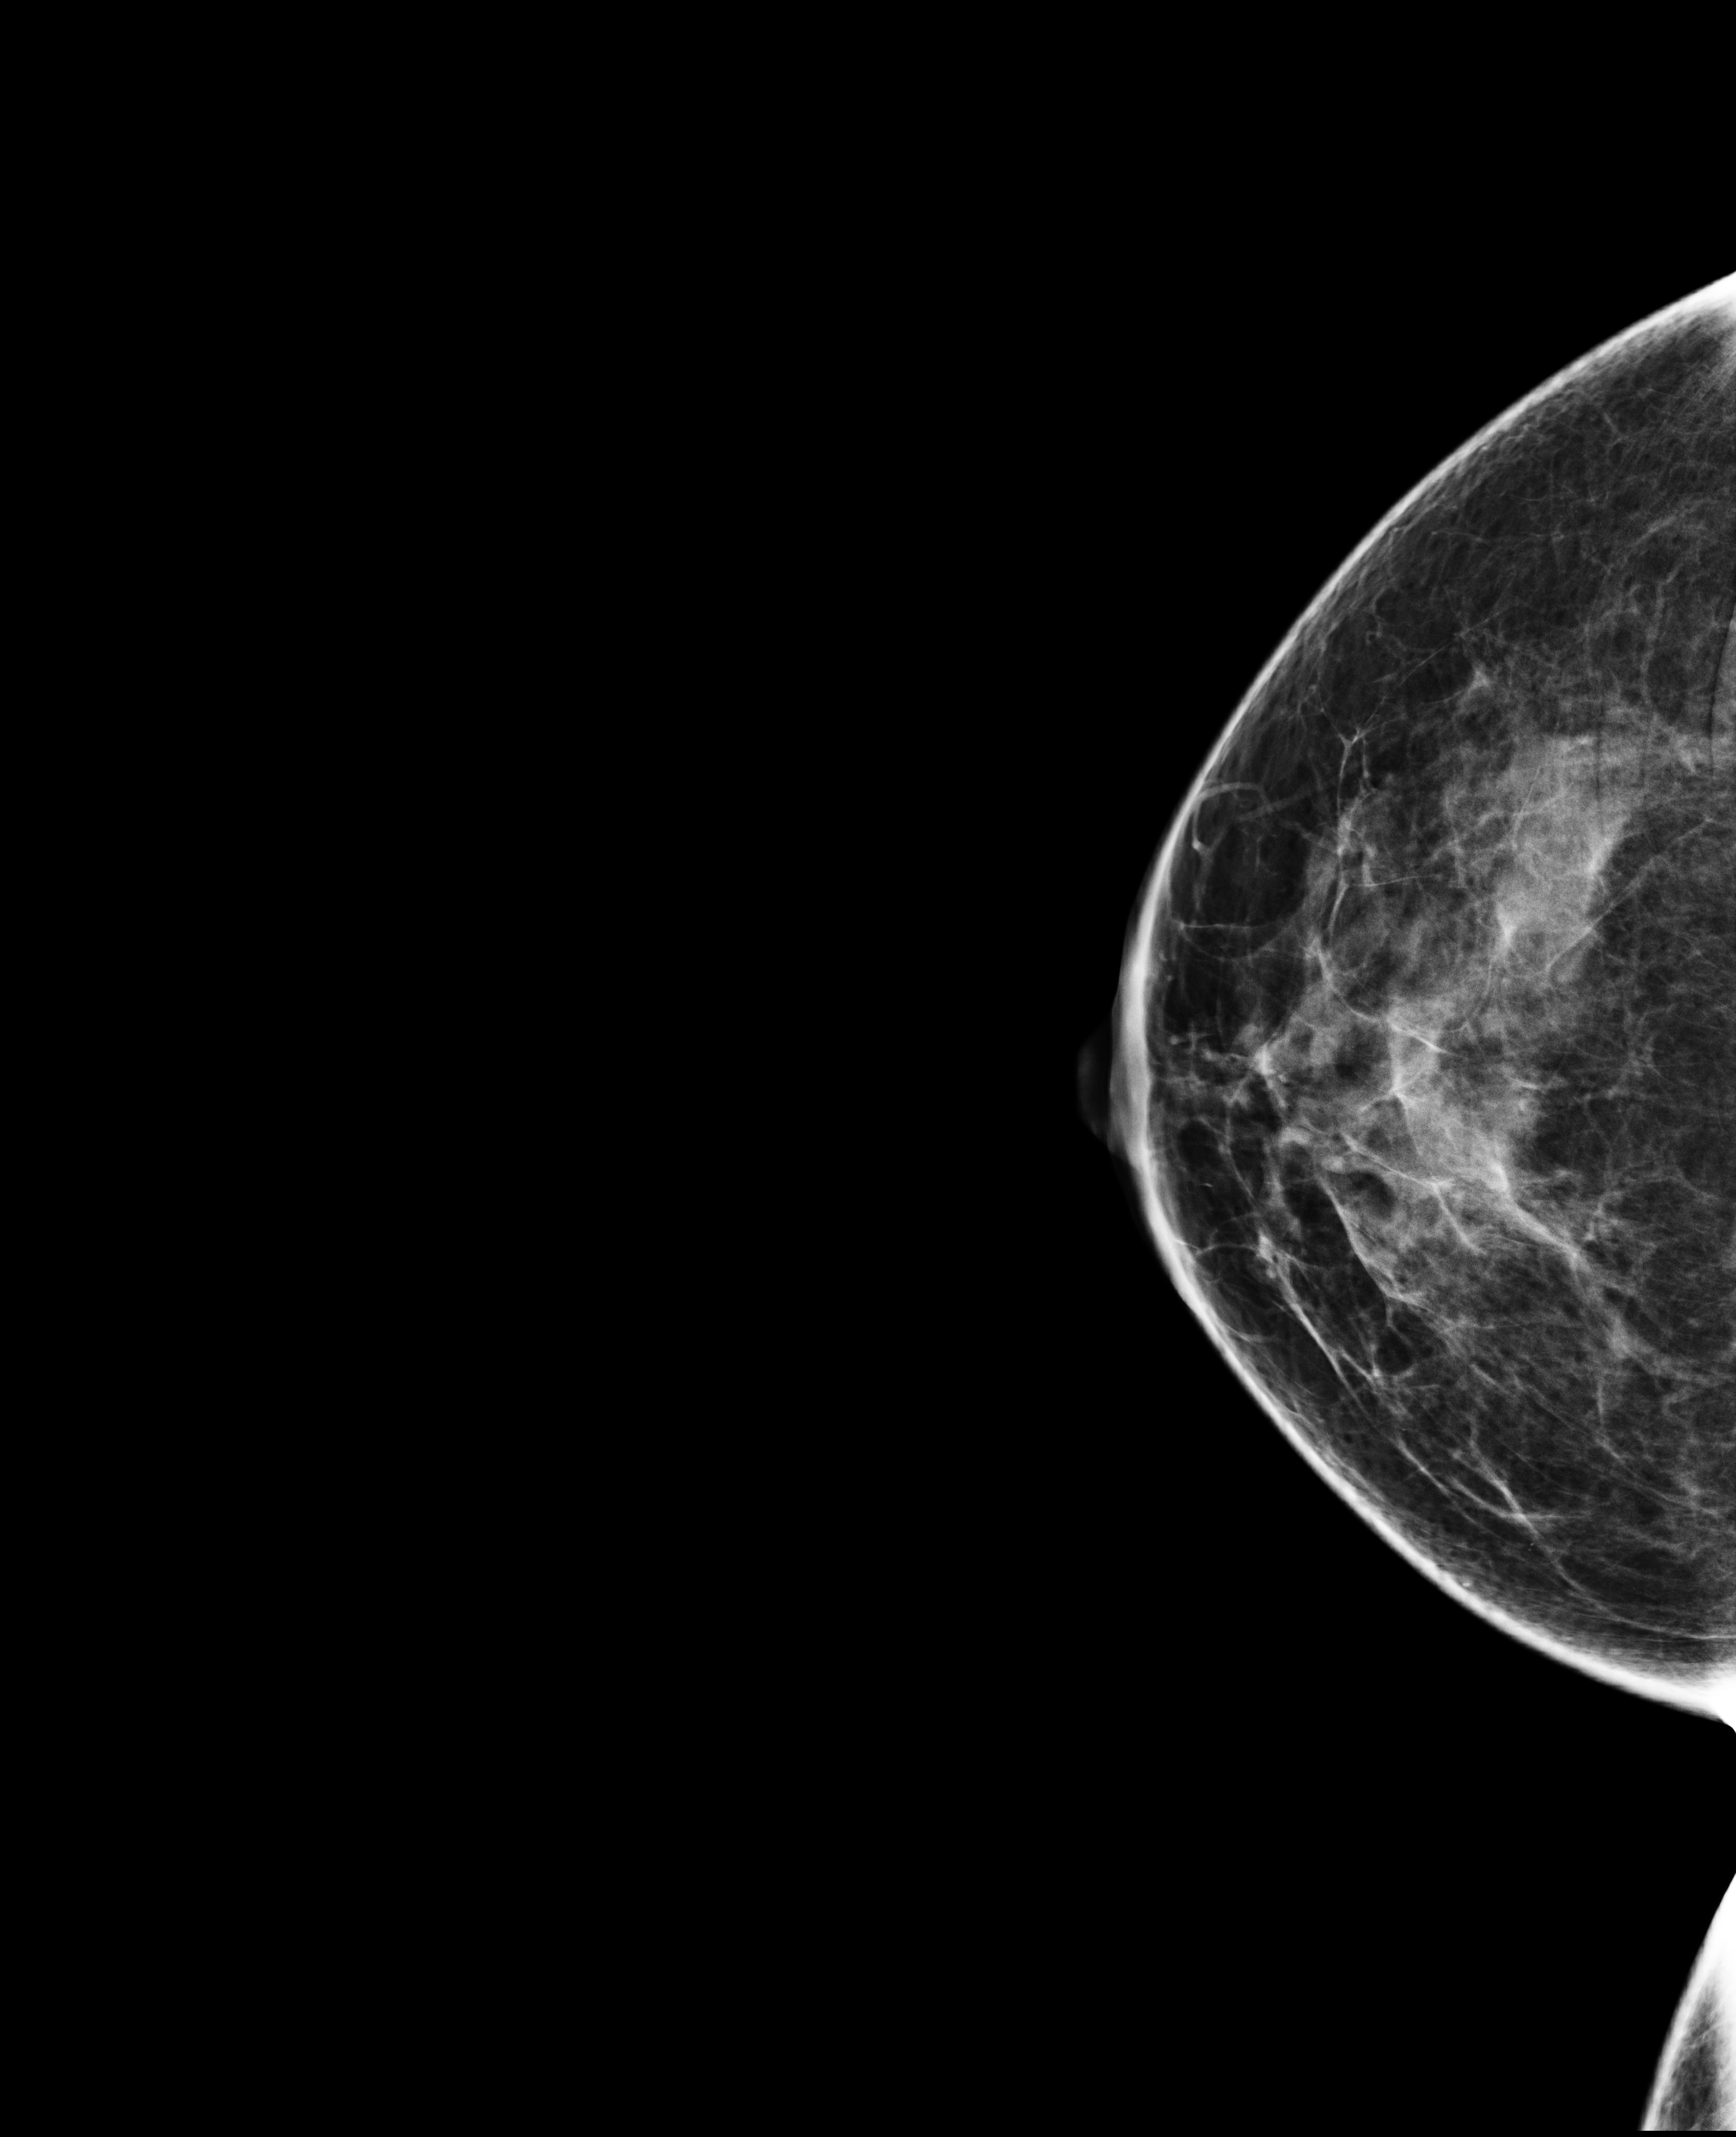
Screening examination; system: Selenia Dimensions. Female patient, age 47 years.
Image type: full-field digital mammogram. Breast: right. Projection: craniocaudal (CC) view.